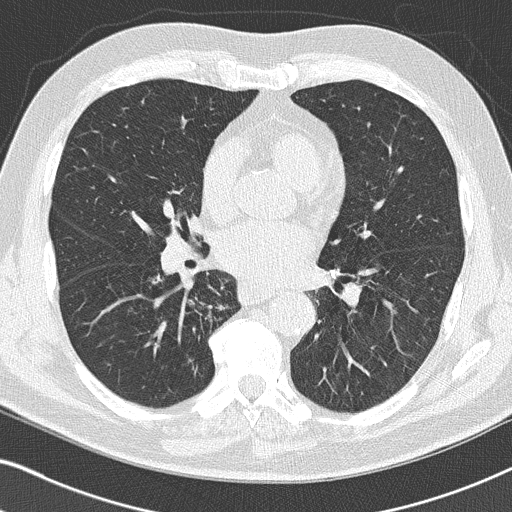
Low-dose screening chest CT, axial slice; third screening round (two years after baseline); lung window (W 1500 / L -600 HU); lung (sharp) reconstruction kernel (B50f); slice 91 of 155 in the series. Male, age 66 years at enrolment. Current smoker at enrolment.
- Lesion marked by an expert reader, bounding box <140,263,230,326> (left, top, right, bottom; pixels).
- The exam's reader record, not a measurement of the box and not confirmed to be the same lesion: non-calcified nodule or mass ≥4 mm, right upper lobe, 5 × 4 mm, smooth margins, pre-existing on the prior screen: yes; interval growth: no.
- Lung cancer was diagnosed 38 days after this screen: squamous cell carcinoma, NOS, right lower lobe, poorly differentiated (G3), stage IIA (AJCC 6th edition), 22 mm at pathology.